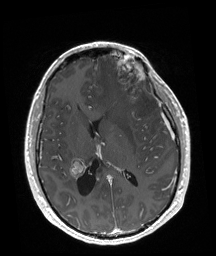
Brain MRI from a brain-tumour surgery series, one axial slice; slice 87 of 192 in the series (ordered by position); T1-weighted post-contrast; 1 mm slice thickness; 216 × 256 image matrix. From the clinical record (not read from this slice): tumour location: Left Frontal.
Outlined on this slice (outlined manually by an expert reader):
- tumour: bounding box (x1, y1, x2, y2) in pixels: (115, 55, 146, 102)